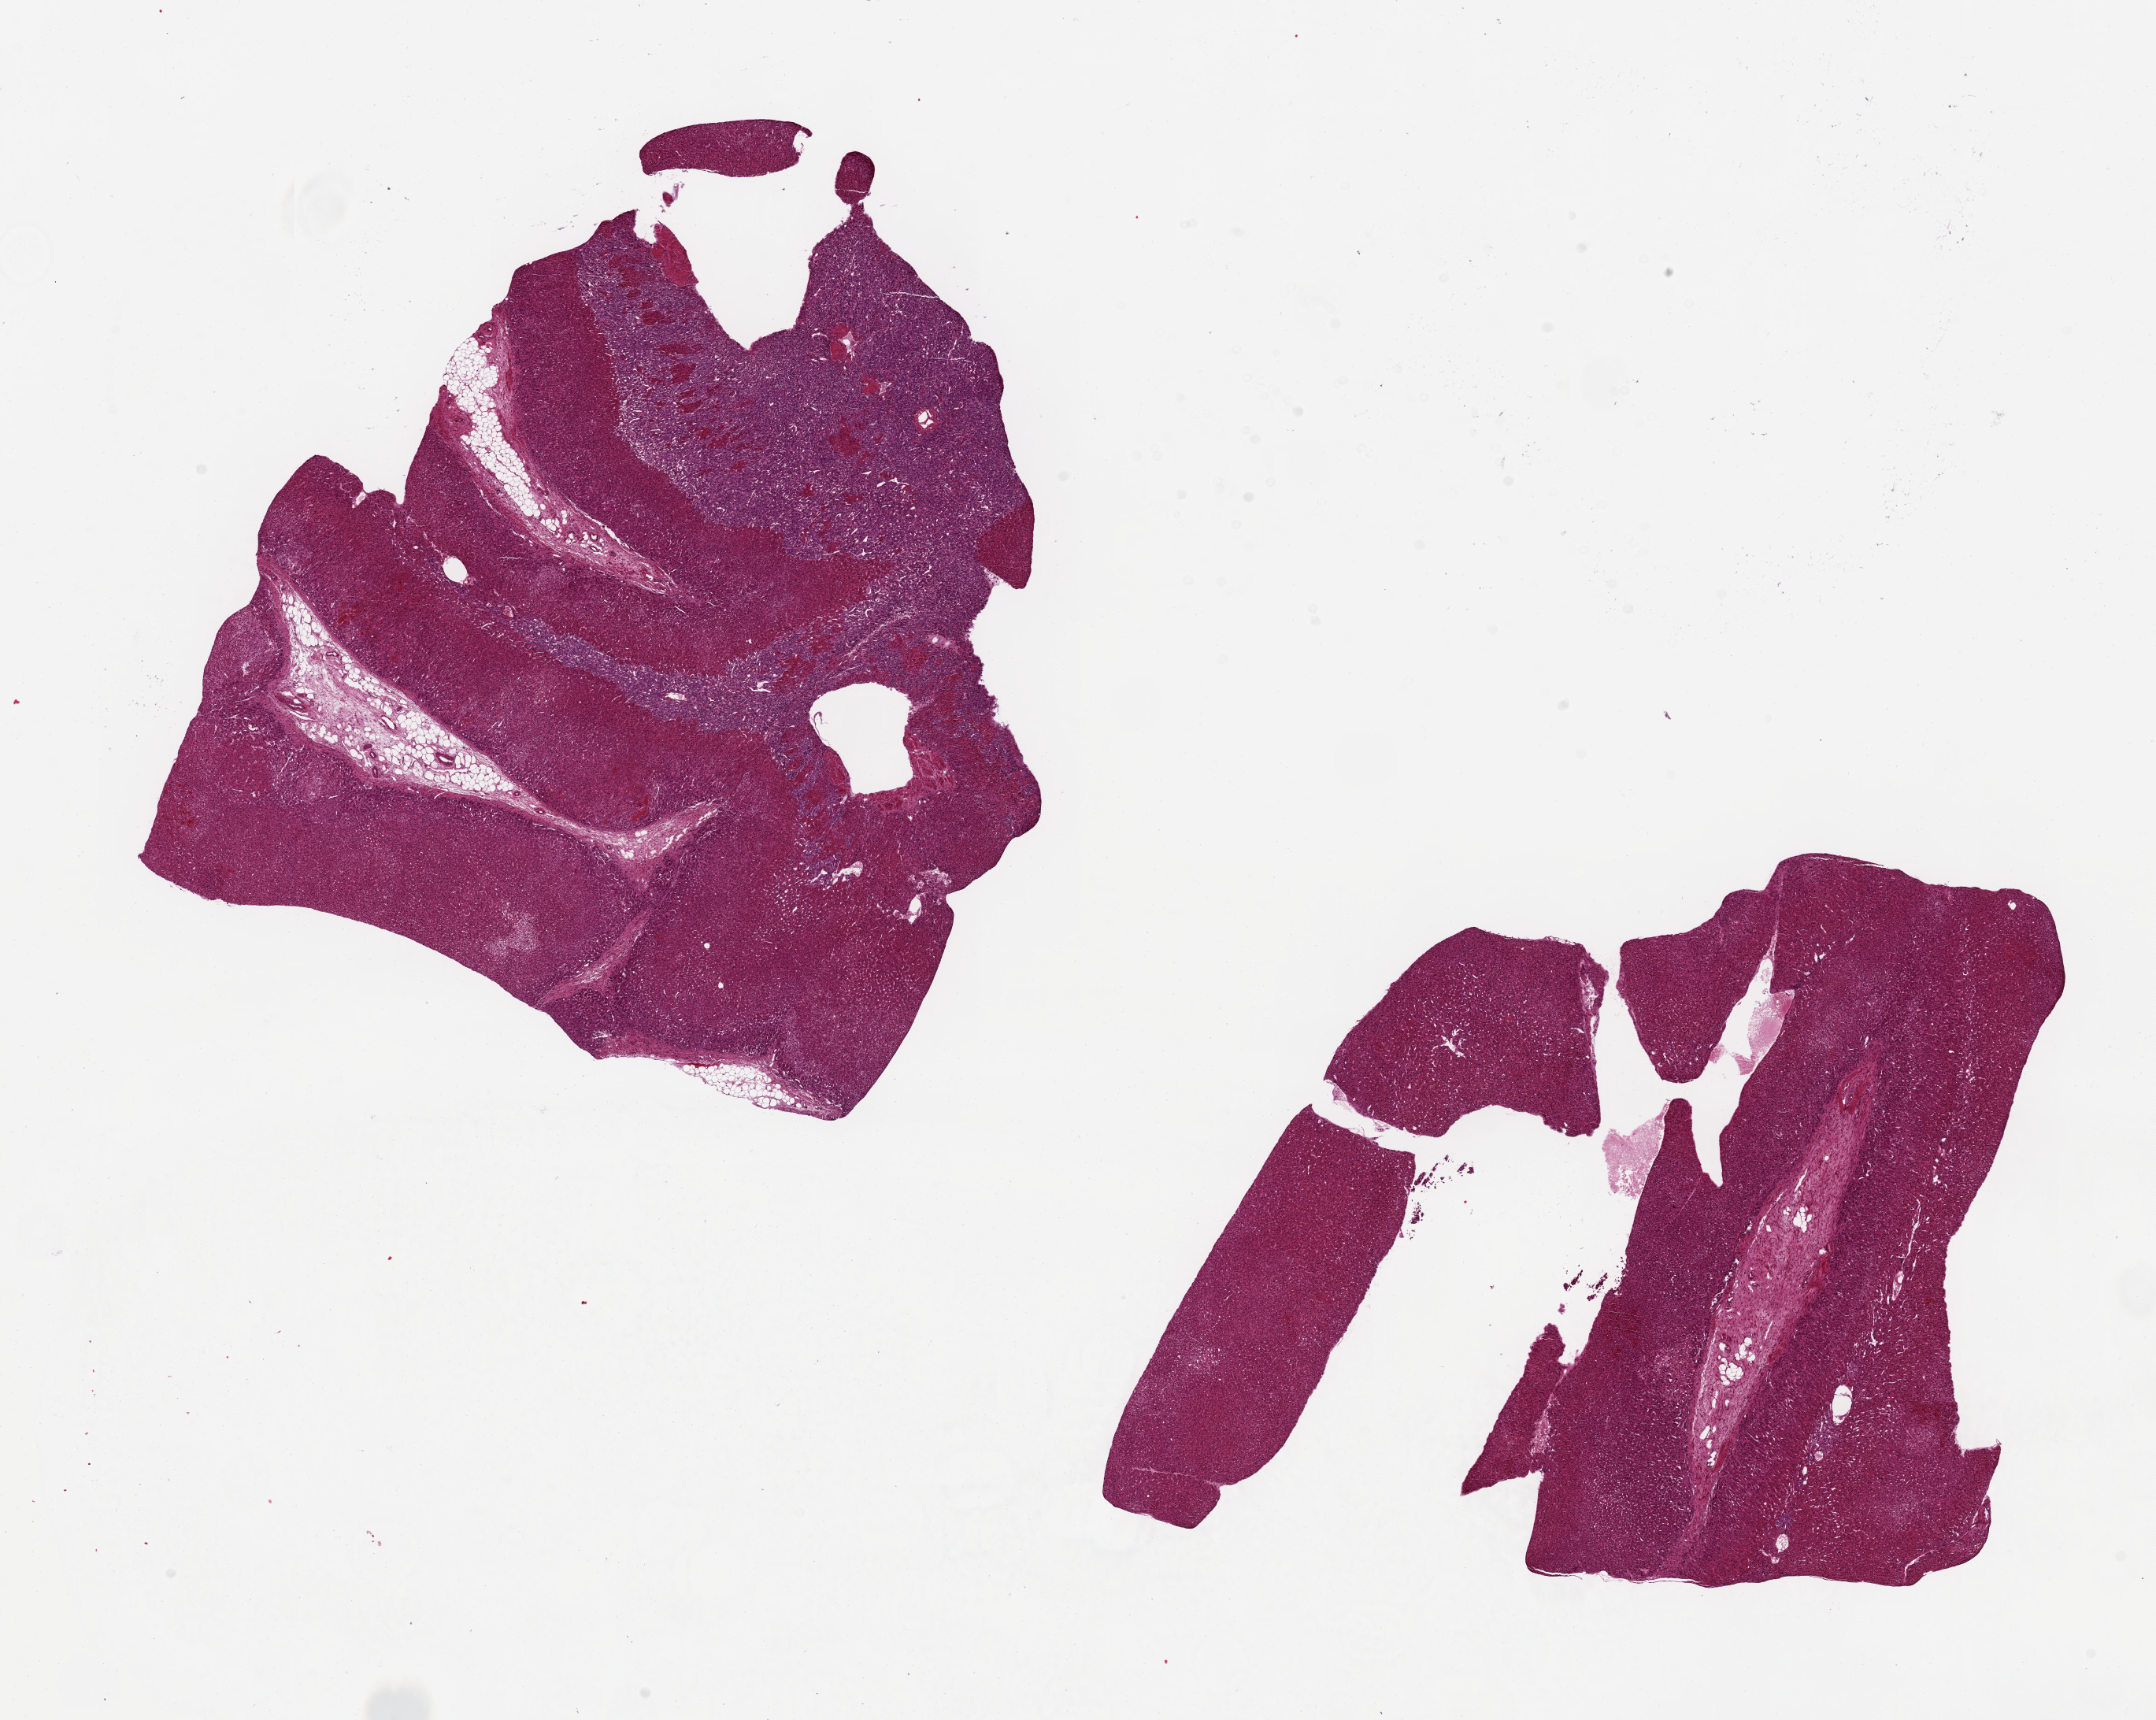
Whole-slide image, hematoxylin and eosin (H&E) stain — low-resolution overview of the scanned area, about 21.7 x 17.3 mm (slide scanned at 20x). PAXgene-fixed, paraffin-embedded tissue. Target tissue: adrenal gland. Tissue donor sample.
Review note (as recorded): 2 aliquots, ~9x7mm. Mainly cortex, 5mm medulla fragment present.